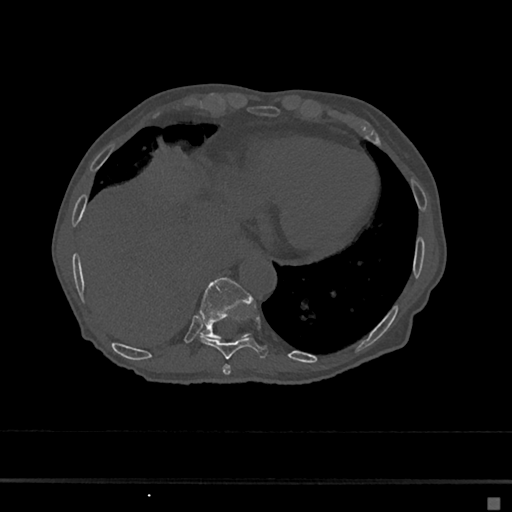
CT including the spine, one axial slice; position 257 of 797 along the scan axis; reconstruction kernel Br40s/3; 120 kVp; bone window (W 1800 / L 400 HU); 0.5 mm slice thickness; 512 × 512 image matrix. Female patient, age 68 years. Case-level facts recorded for this patient, not image findings: primary cancer: renal.
Outlined on this slice (semi-automatically segmented with operator editing):
- T10 vertebra: box from (x=200, y=278) to (x=252, y=339) px
- T8 vertebra: (x=222, y=364)–(x=231, y=375)
- T9 vertebra: (x=200, y=315)–(x=269, y=359)